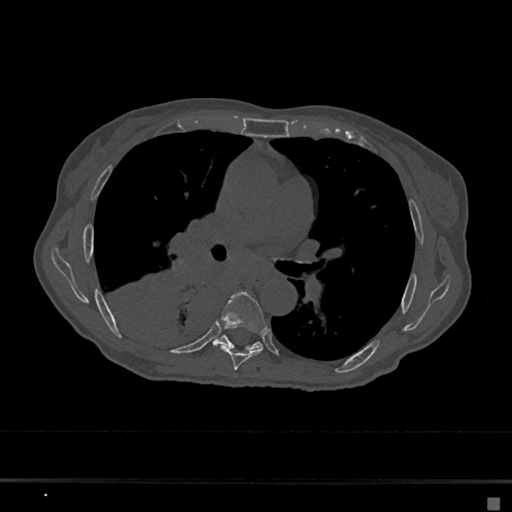
CT including the spine, one axial slice. Position 401 of 797 along the scan axis. Bone window (W 1800 / L 400 HU). 0.5 mm slice thickness. 512 × 512 image matrix. Patient: female, 68 years. Case-level facts recorded for this patient, not image findings: primary cancer: renal.
Structures marked on this image (semi-automatic segmentation, software-assisted and operator-edited):
- T6 vertebra: bounding box [x1, y1, x2, y2] px = [219, 291, 268, 370]
- T7 vertebra: [215, 336, 262, 351]